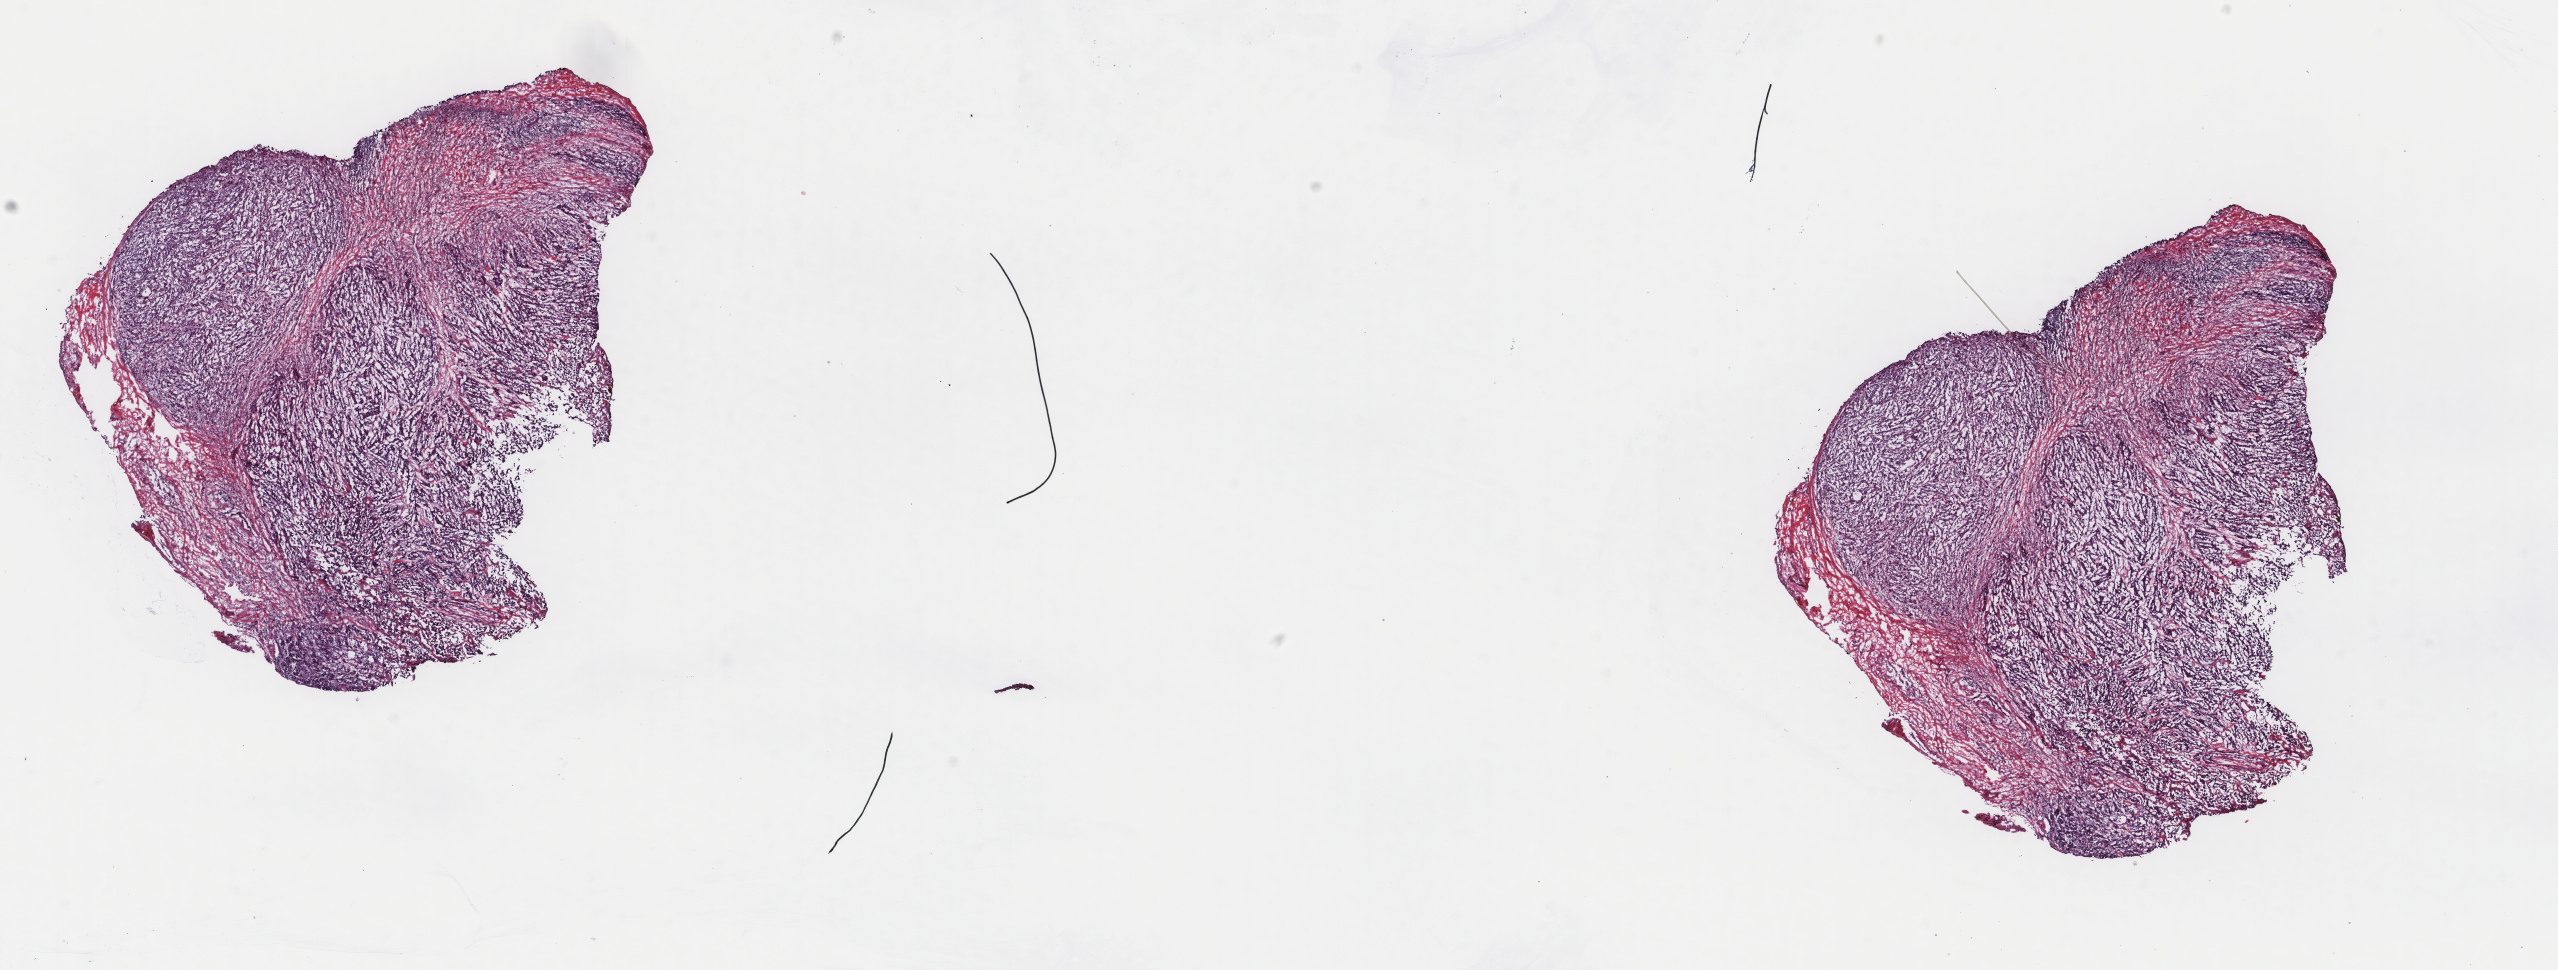
Digitized H&E-stained tissue section (whole slide), whole scanned area (about 20.3 x 7.7 mm, acquisition: 40x scan) shown as a low-resolution overview, frozen section from the top of the tissue portion, metastatic tumour sample, sampled site: lymph nodes of head, face and neck. Patient: male, age at initial diagnosis 68 years. Composition of this section per pathologist review: tumour cells 80%, tumour nuclei 80%, normal cells 0%, stromal cells 20%, necrosis 0%. Infiltration values recorded for this section: lymphocyte infiltration 0%, monocyte infiltration 0%, neutrophil infiltration 0%.
This section: metastatic tumour tissue. Patient diagnosis: Malignant melanoma, NOS.